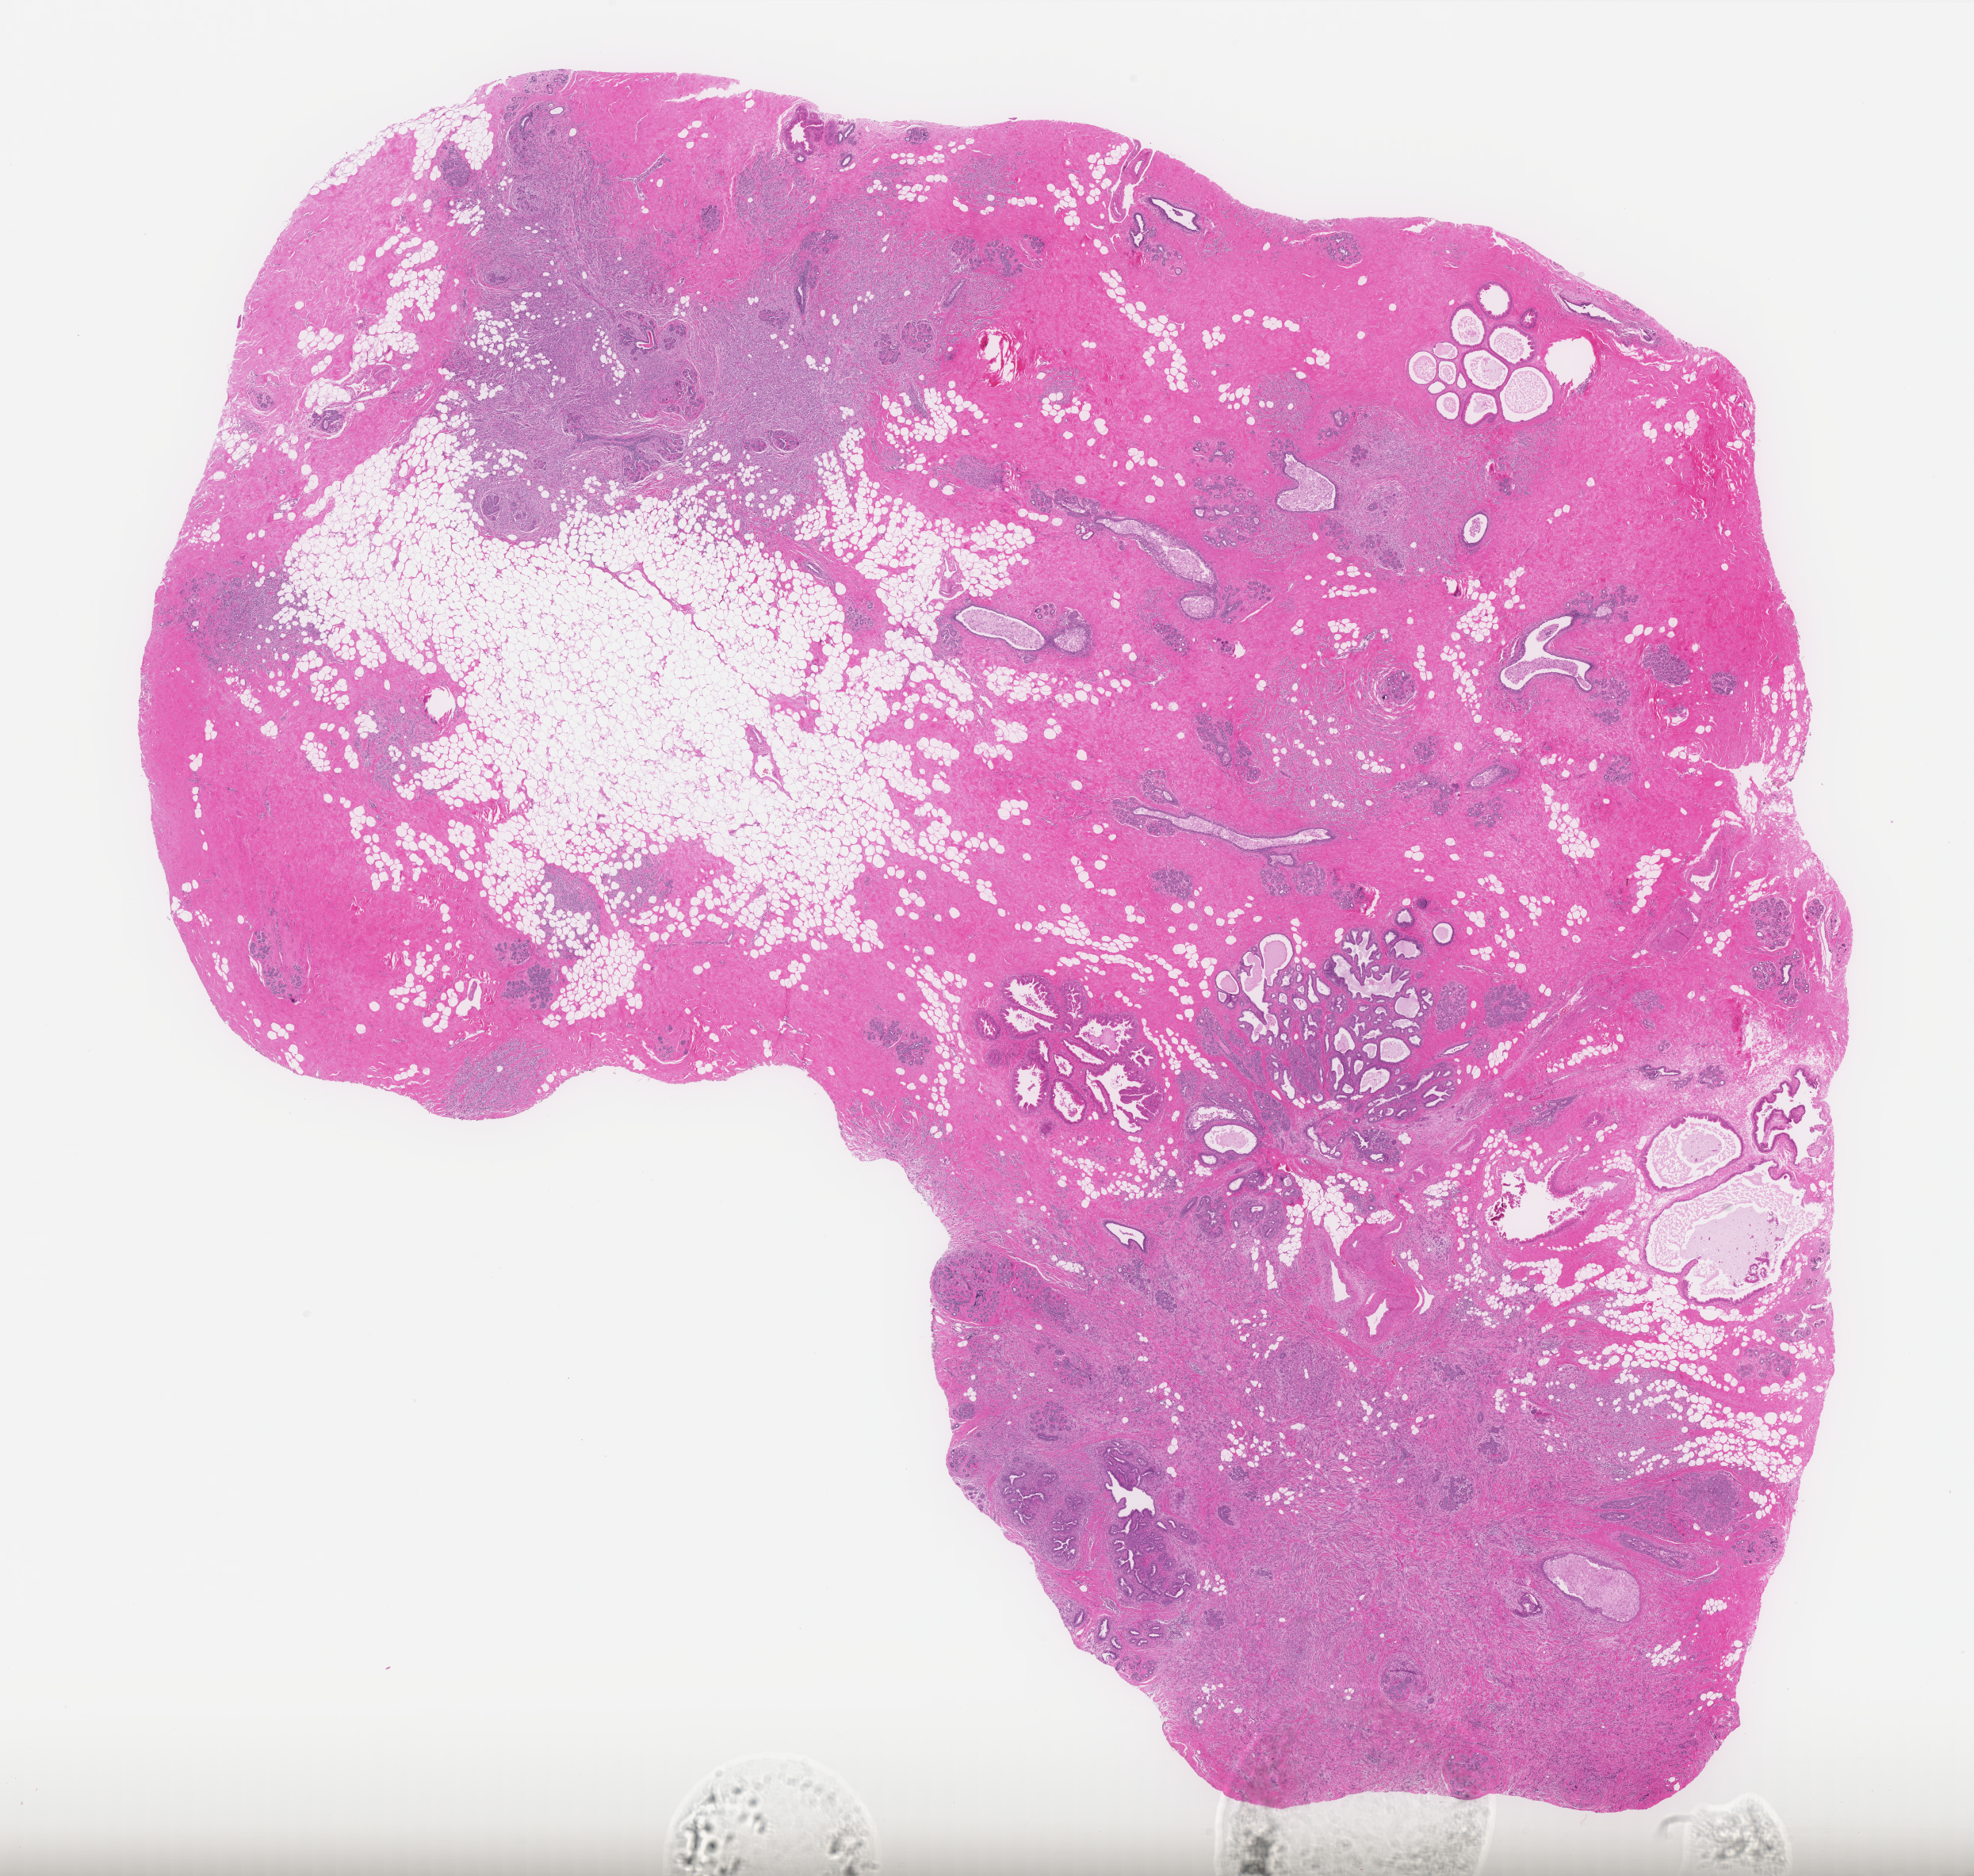
Digitized H&E tissue section (whole slide), shown as a low-resolution overview of the whole scanned area (about 20.0 x 19.0 mm), formalin-fixed paraffin-embedded (FFPE) diagnostic section, sample: primary tumour, breast. Patient: female, age at initial diagnosis 48 years.
- AJCC pathologic stage: IIIA
- diagnosis: Lobular carcinoma, NOS
- lymph nodes positive (case pathology): 4 of 29 examined